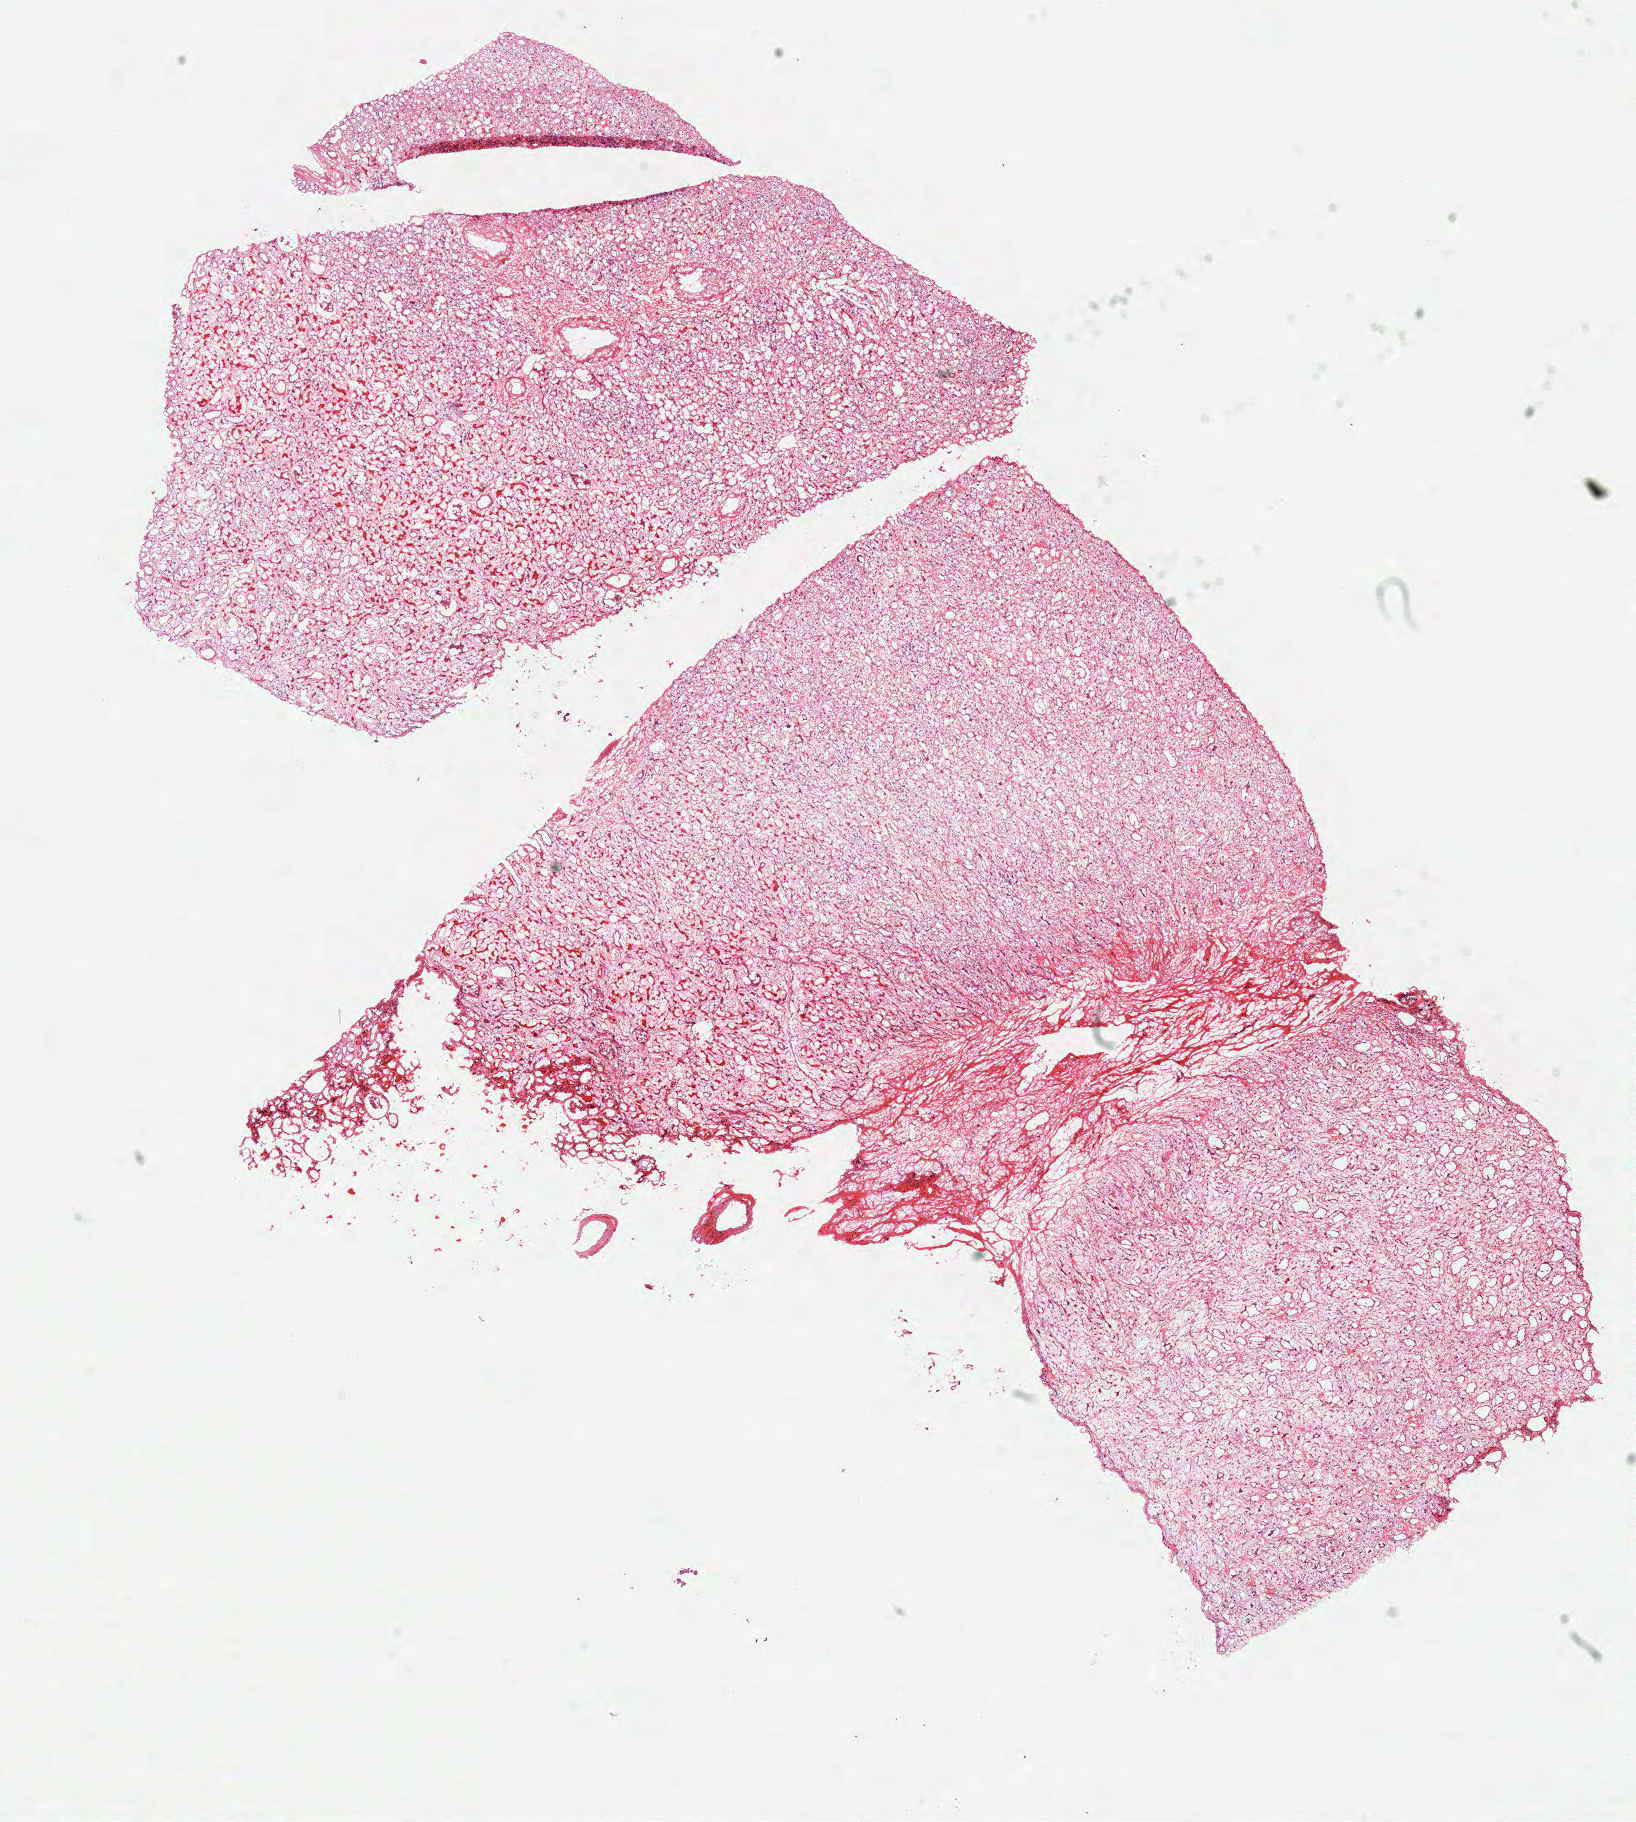
Digitized Hematoxylin and eosin (H&E) stained tissue section (whole slide), low-resolution overview of the scanned area, about 12.9 x 14.4 mm (from a 40x scan). Frozen section from the top of the tissue portion. Kidney, solid tissue normal (non-tumour tissue) sample. Male patient; age at initial diagnosis 60 years.
This section: solid tissue normal (non-tumour) sample from the same patient. Patient diagnosis: Clear cell adenocarcinoma, NOS.